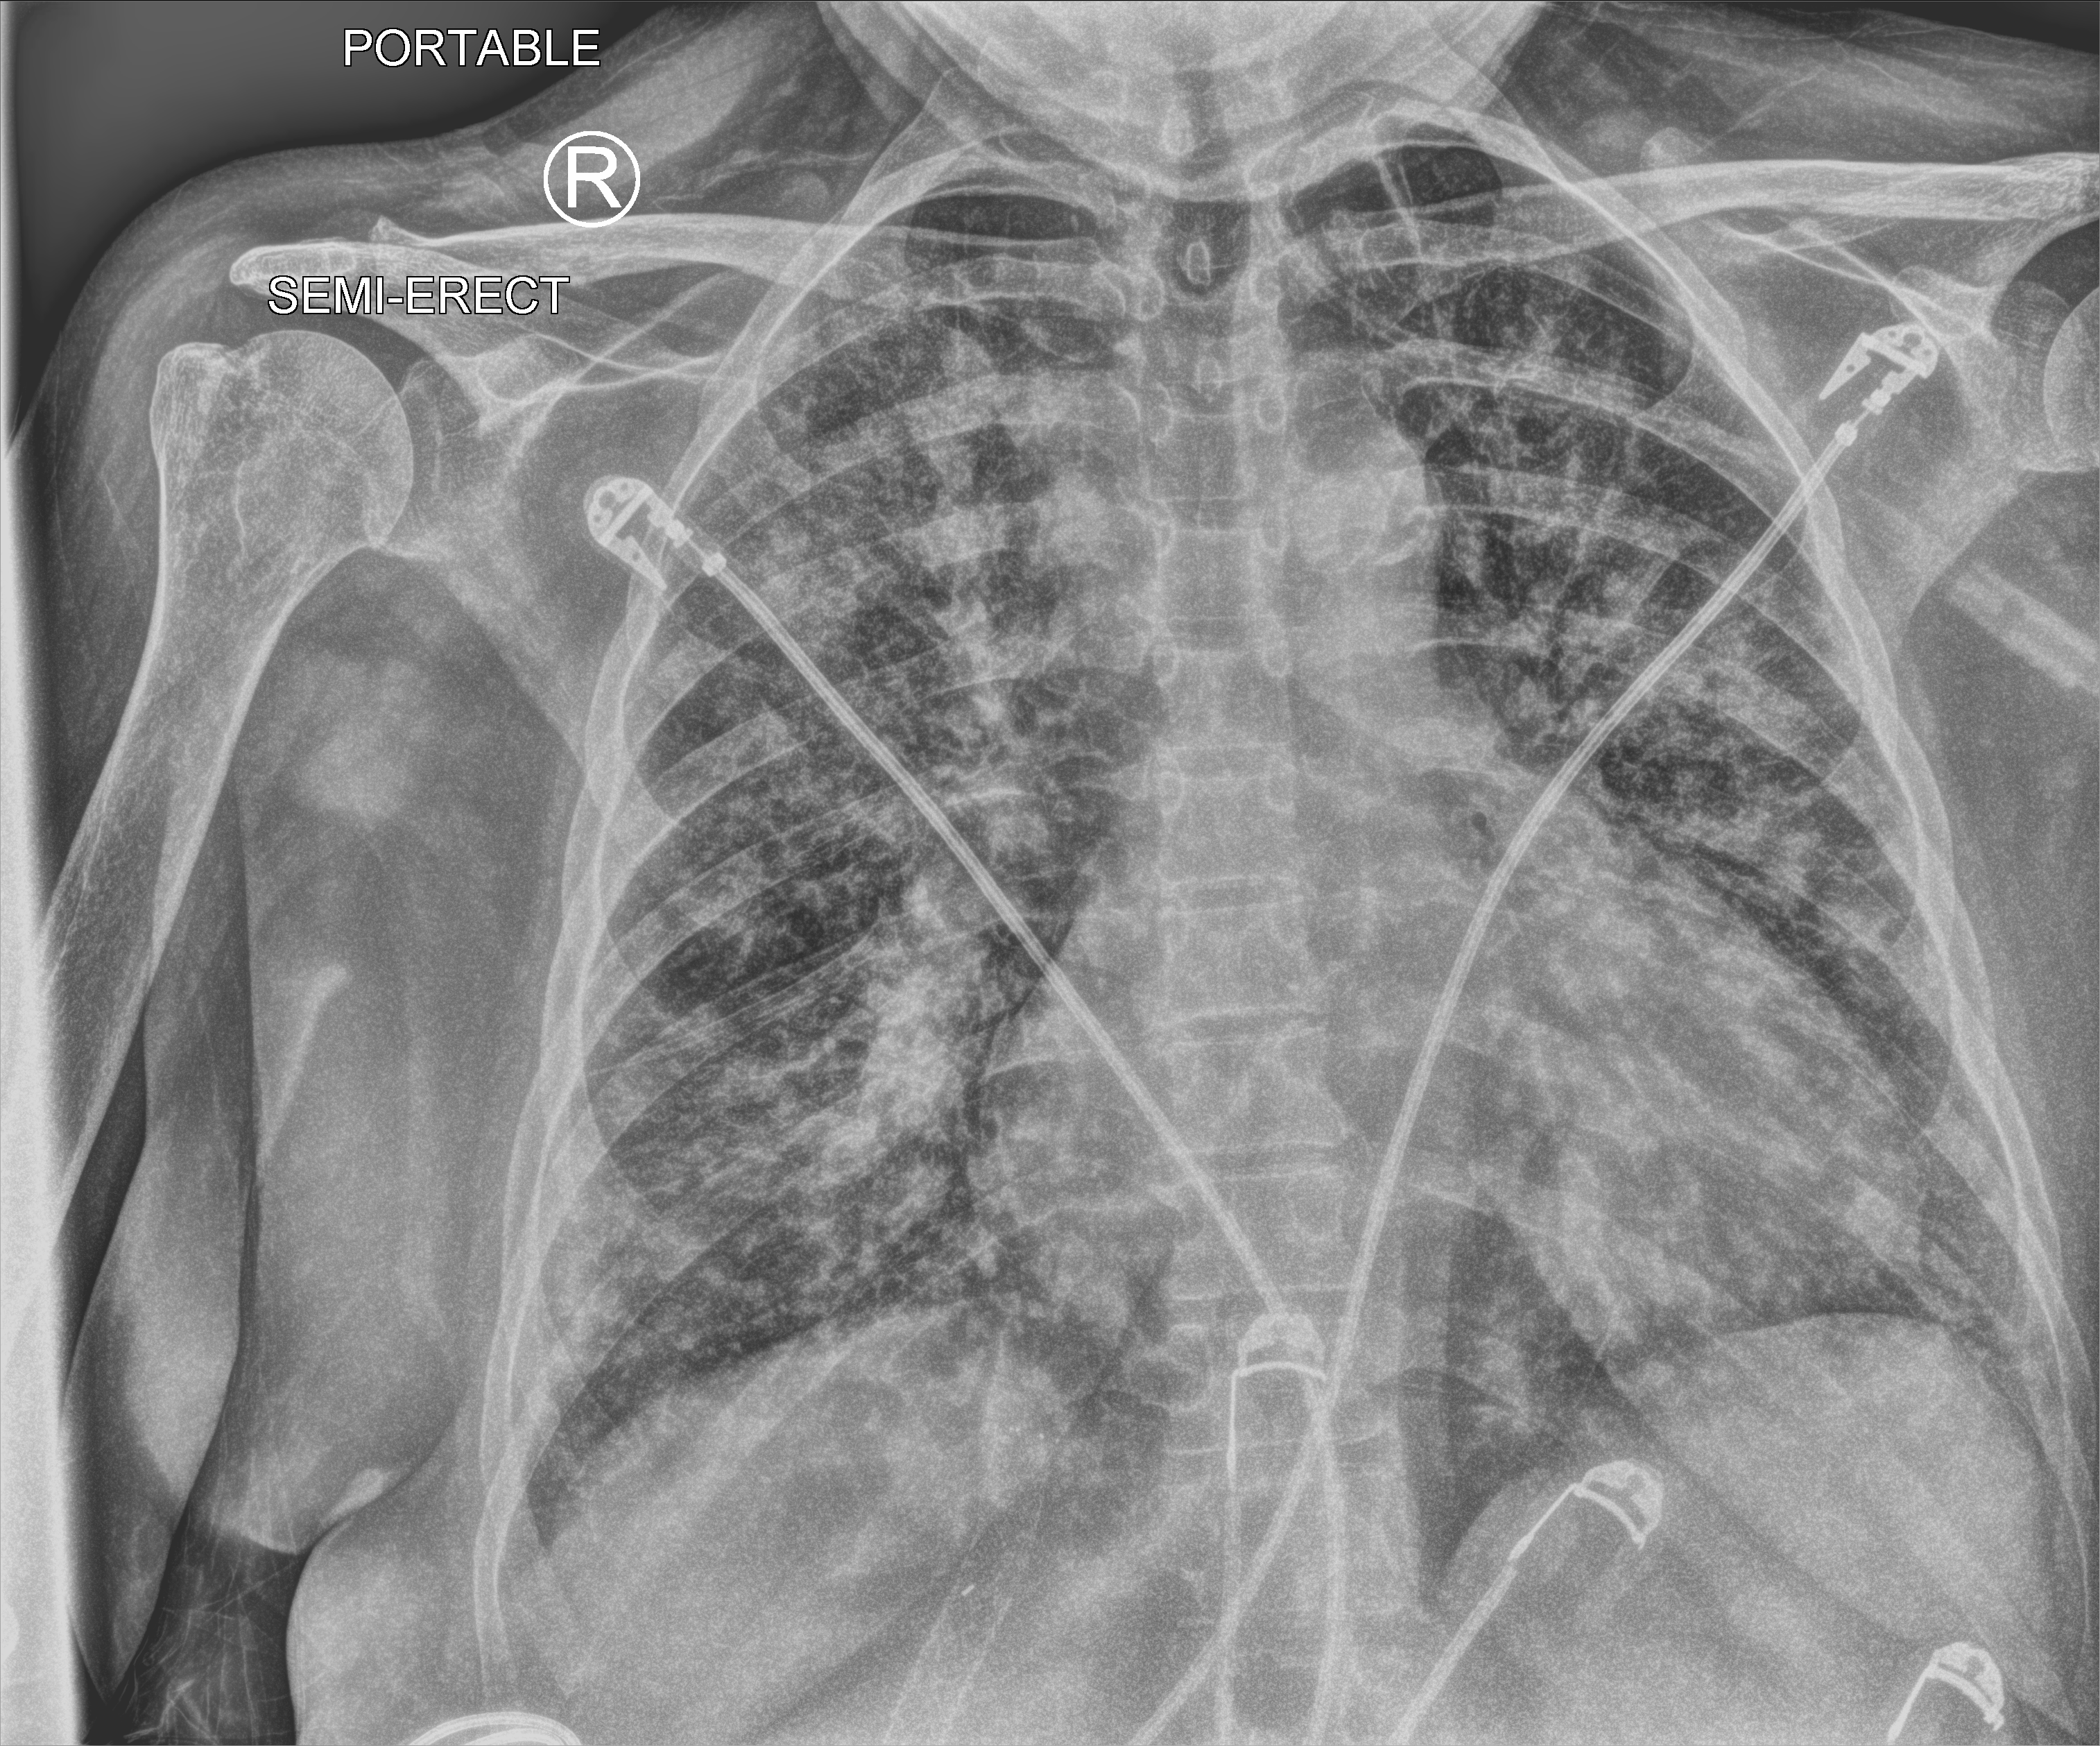
Bedside chest radiograph (computed radiography); anteroposterior (AP) projection. Female patient hospitalised with COVID-19, age 60–74 years.
Hospital-stay facts (about this admission, not read from this image; timing relative to this image not recorded): smoking status (admission record): never; admitted to intensive care during this hospital stay: yes; mechanically ventilated during this hospital stay: no.